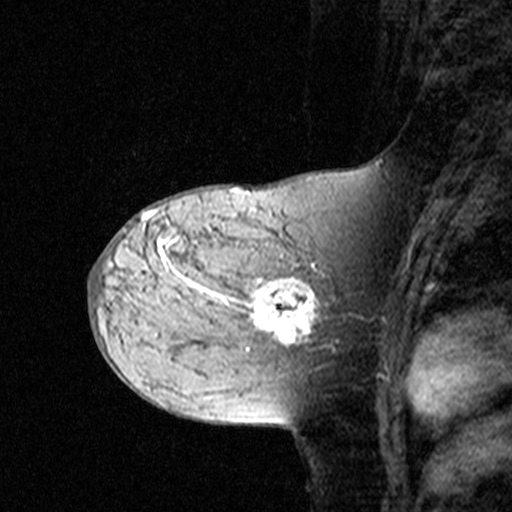
Breast MRI (dynamic contrast-enhanced), one sagittal slice; dynamic contrast-enhanced study with each time point stored as its own series, time point 2 of 3 at this slice position (early post-contrast, ordered by acquisition time); 1.5 T; TE 4.5 ms, TR 11 ms; 512 × 512 image matrix, field of view 200 × 200 mm. Female patient, age 44 years. Case-level facts recorded for this patient, not image findings: setting: breast cancer imaged before/during neoadjuvant chemotherapy; receptor status: triple-negative.
Structures marked on this image (semi-automatically segmented with operator editing):
- analysis volume of interest (the breast-tissue region the enhancement analysis was run in; not a lesion): box from (x=142, y=208) to (x=349, y=363) px
- tumour enhancement mask (voxels above the 90 % enhancement threshold inside the analysis volume of interest): (x=142, y=210)–(x=317, y=345)